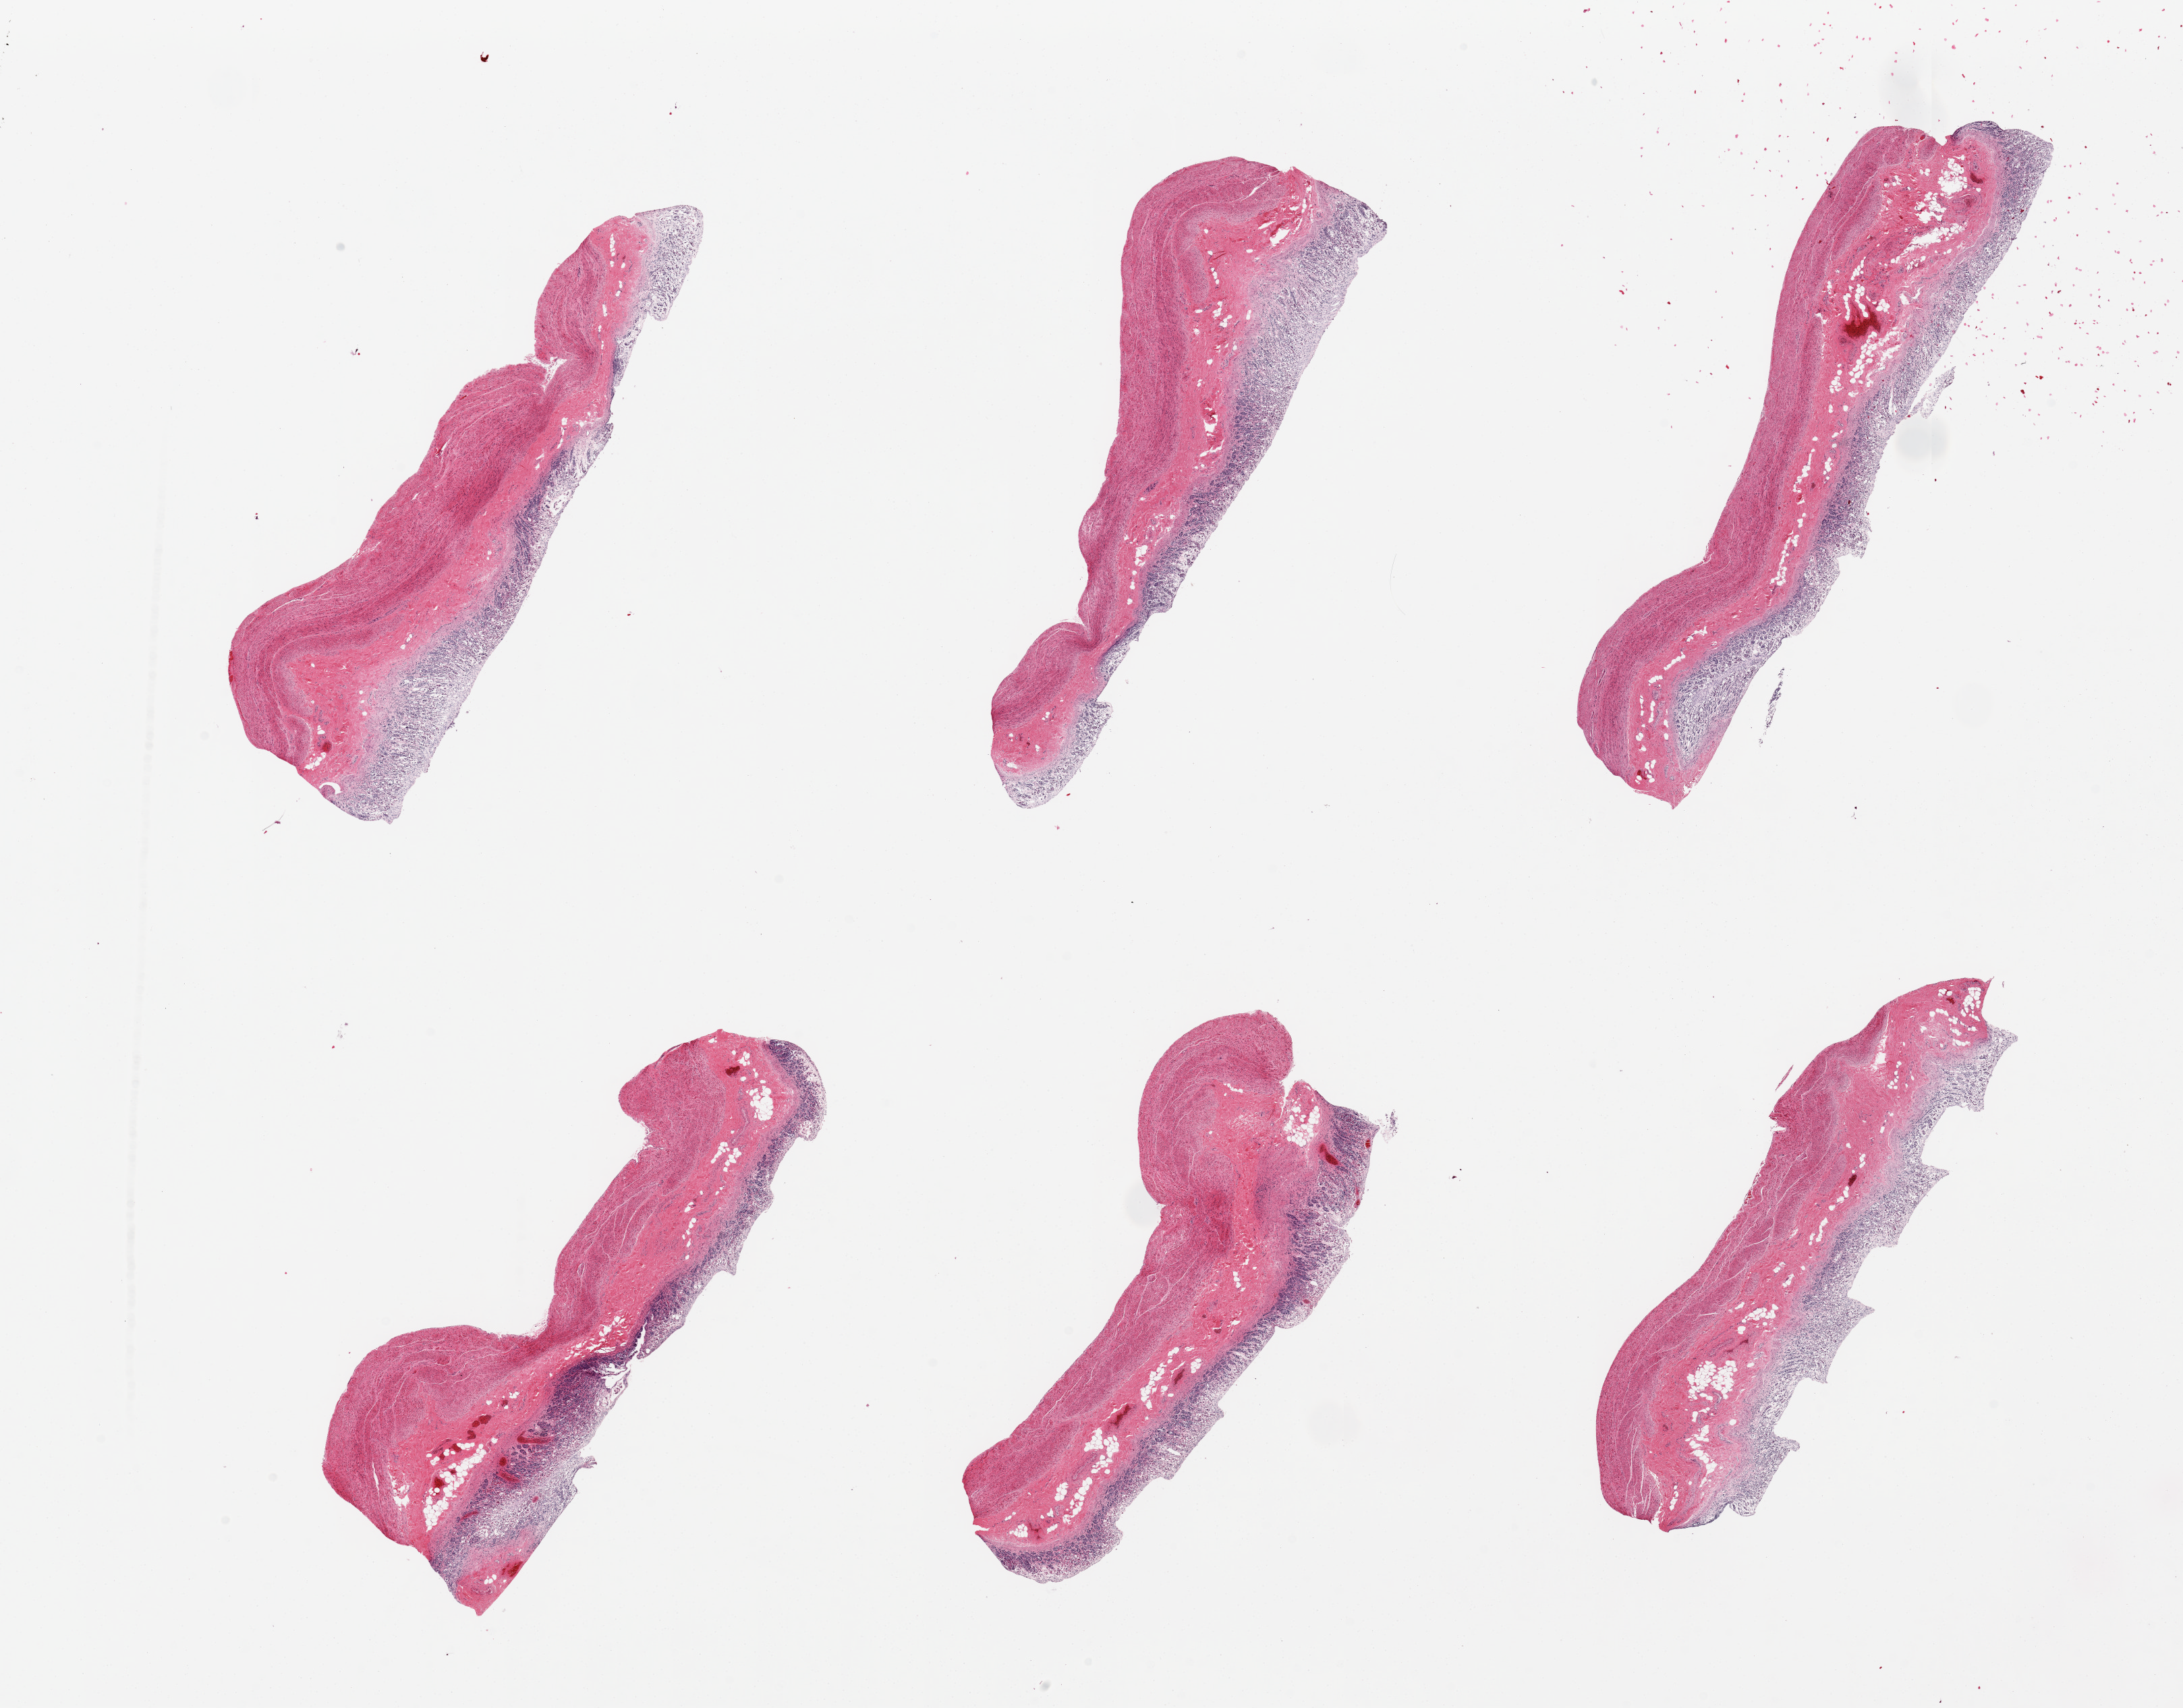
Whole-slide image, H&E stain, brightfield, shown as a low-resolution overview of the whole scanned area (about 25.6 x 20.0 mm), PAXgene-fixed paraffin-embedded (PFPE) section, section of stomach (target tissue), donor tissue sample. Donor: male.
Review note (as recorded): 6 pieces; mucosa totally autolyzed, muscle is moderately autolyzed.